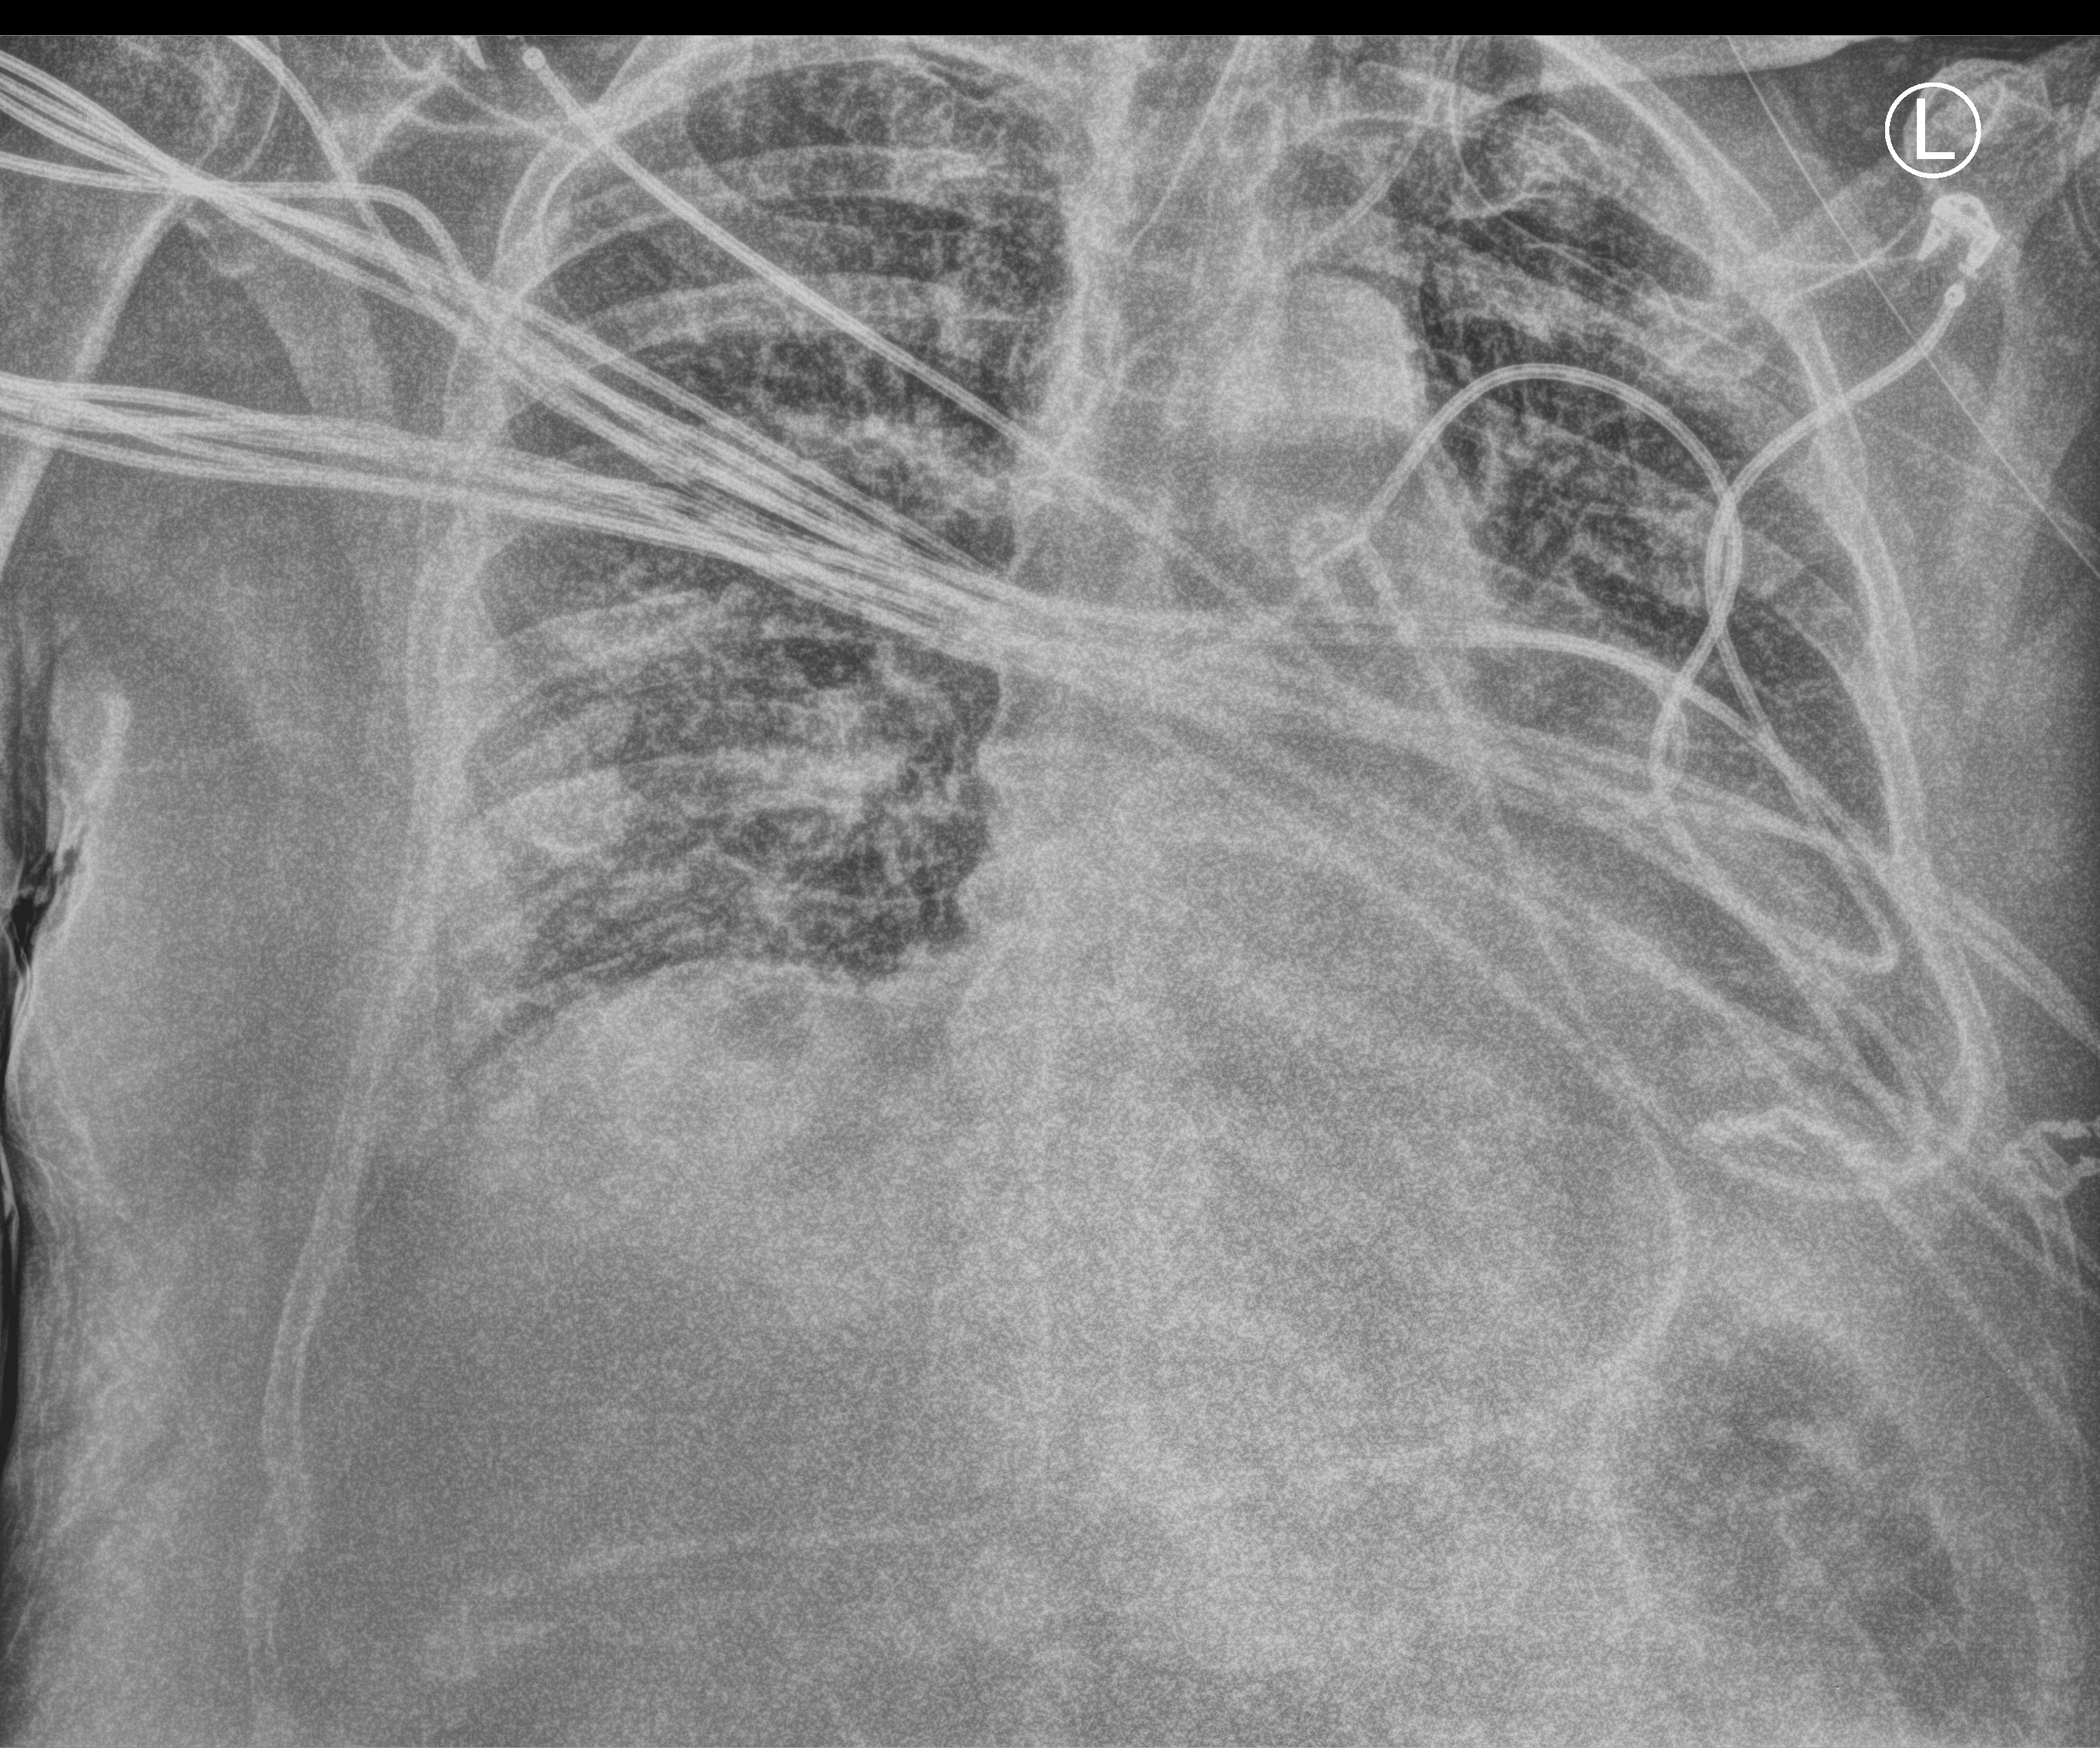
Portable chest radiograph; anteroposterior (AP) projection. Male patient hospitalised with COVID-19, age 75–90 years.
Admission-level facts for this patient (not findings on this image; timing relative to this image not recorded): admitted to intensive care during this hospital stay: yes; chronic kidney disease (admission record): no.